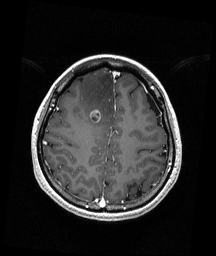
Brain MRI from a brain-tumour surgery series, one axial slice; slice 56 of 192 in the series (ordered by position); T1-weighted post-contrast; 1 mm slice thickness; 216 × 256 image matrix, field of view 211 × 250 mm. Case-level facts recorded for this patient, not image findings: histopathology: Astrocytoma; WHO grade: 4; IDH mutation: yes; tumour location: Right Frontal.
Outlined on this slice (expert manual segmentation):
- tumour: bounding box <91,109,101,123> (left, top, right, bottom; pixels)